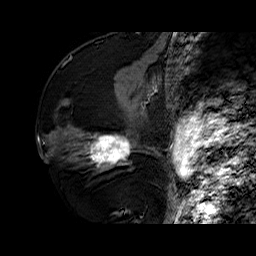
Breast MRI (dynamic contrast-enhanced), one sagittal slice; dynamic contrast-enhanced series, time point 2 of 6 at this slice position (early post-contrast); 1.5 T; TE 6.4 ms, TR 32.7 ms; 4 mm slice thickness; 256 × 256 image matrix, field of view 200 × 200 mm. Female patient. Case-level facts recorded for this patient, not image findings: setting: breast cancer imaged before/during neoadjuvant chemotherapy; receptor status: HR-positive, HER2-negative.
Outlined on this slice (semi-automatically segmented with operator editing):
- analysis volume of interest (the breast-tissue region the enhancement analysis was run in; not a lesion): box from (x=73, y=110) to (x=141, y=173) px
- tumour enhancement mask (voxels above the 100 % enhancement threshold inside the analysis volume of interest): (x=88, y=135)–(x=132, y=166)